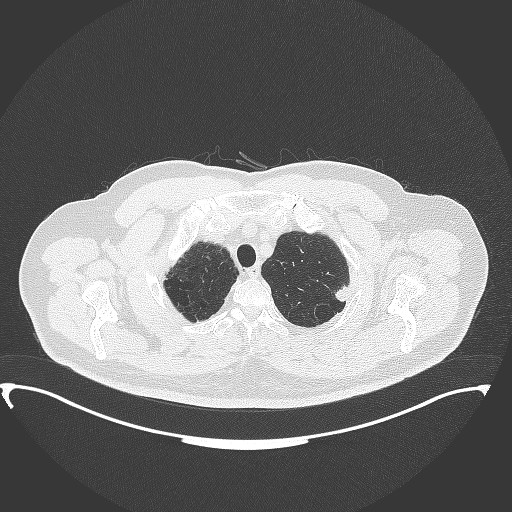
Chest CT, one axial slice; slice 326 of 350 in the series (ordered by position); reconstruction kernel B70f; lung window (W 1500 / L -600 HU); 512 × 512 image matrix. Patient: male, 64 years. From the clinical record (not read from this slice): clinical TNM (as recorded): T1c N1 M1.
Annotated regions visible in this slice (bounding box drawn by a radiologist):
- lung tumour (recorded histology: adenocarcinoma): bounding box (x1, y1, x2, y2) in pixels: (333, 281, 355, 311)